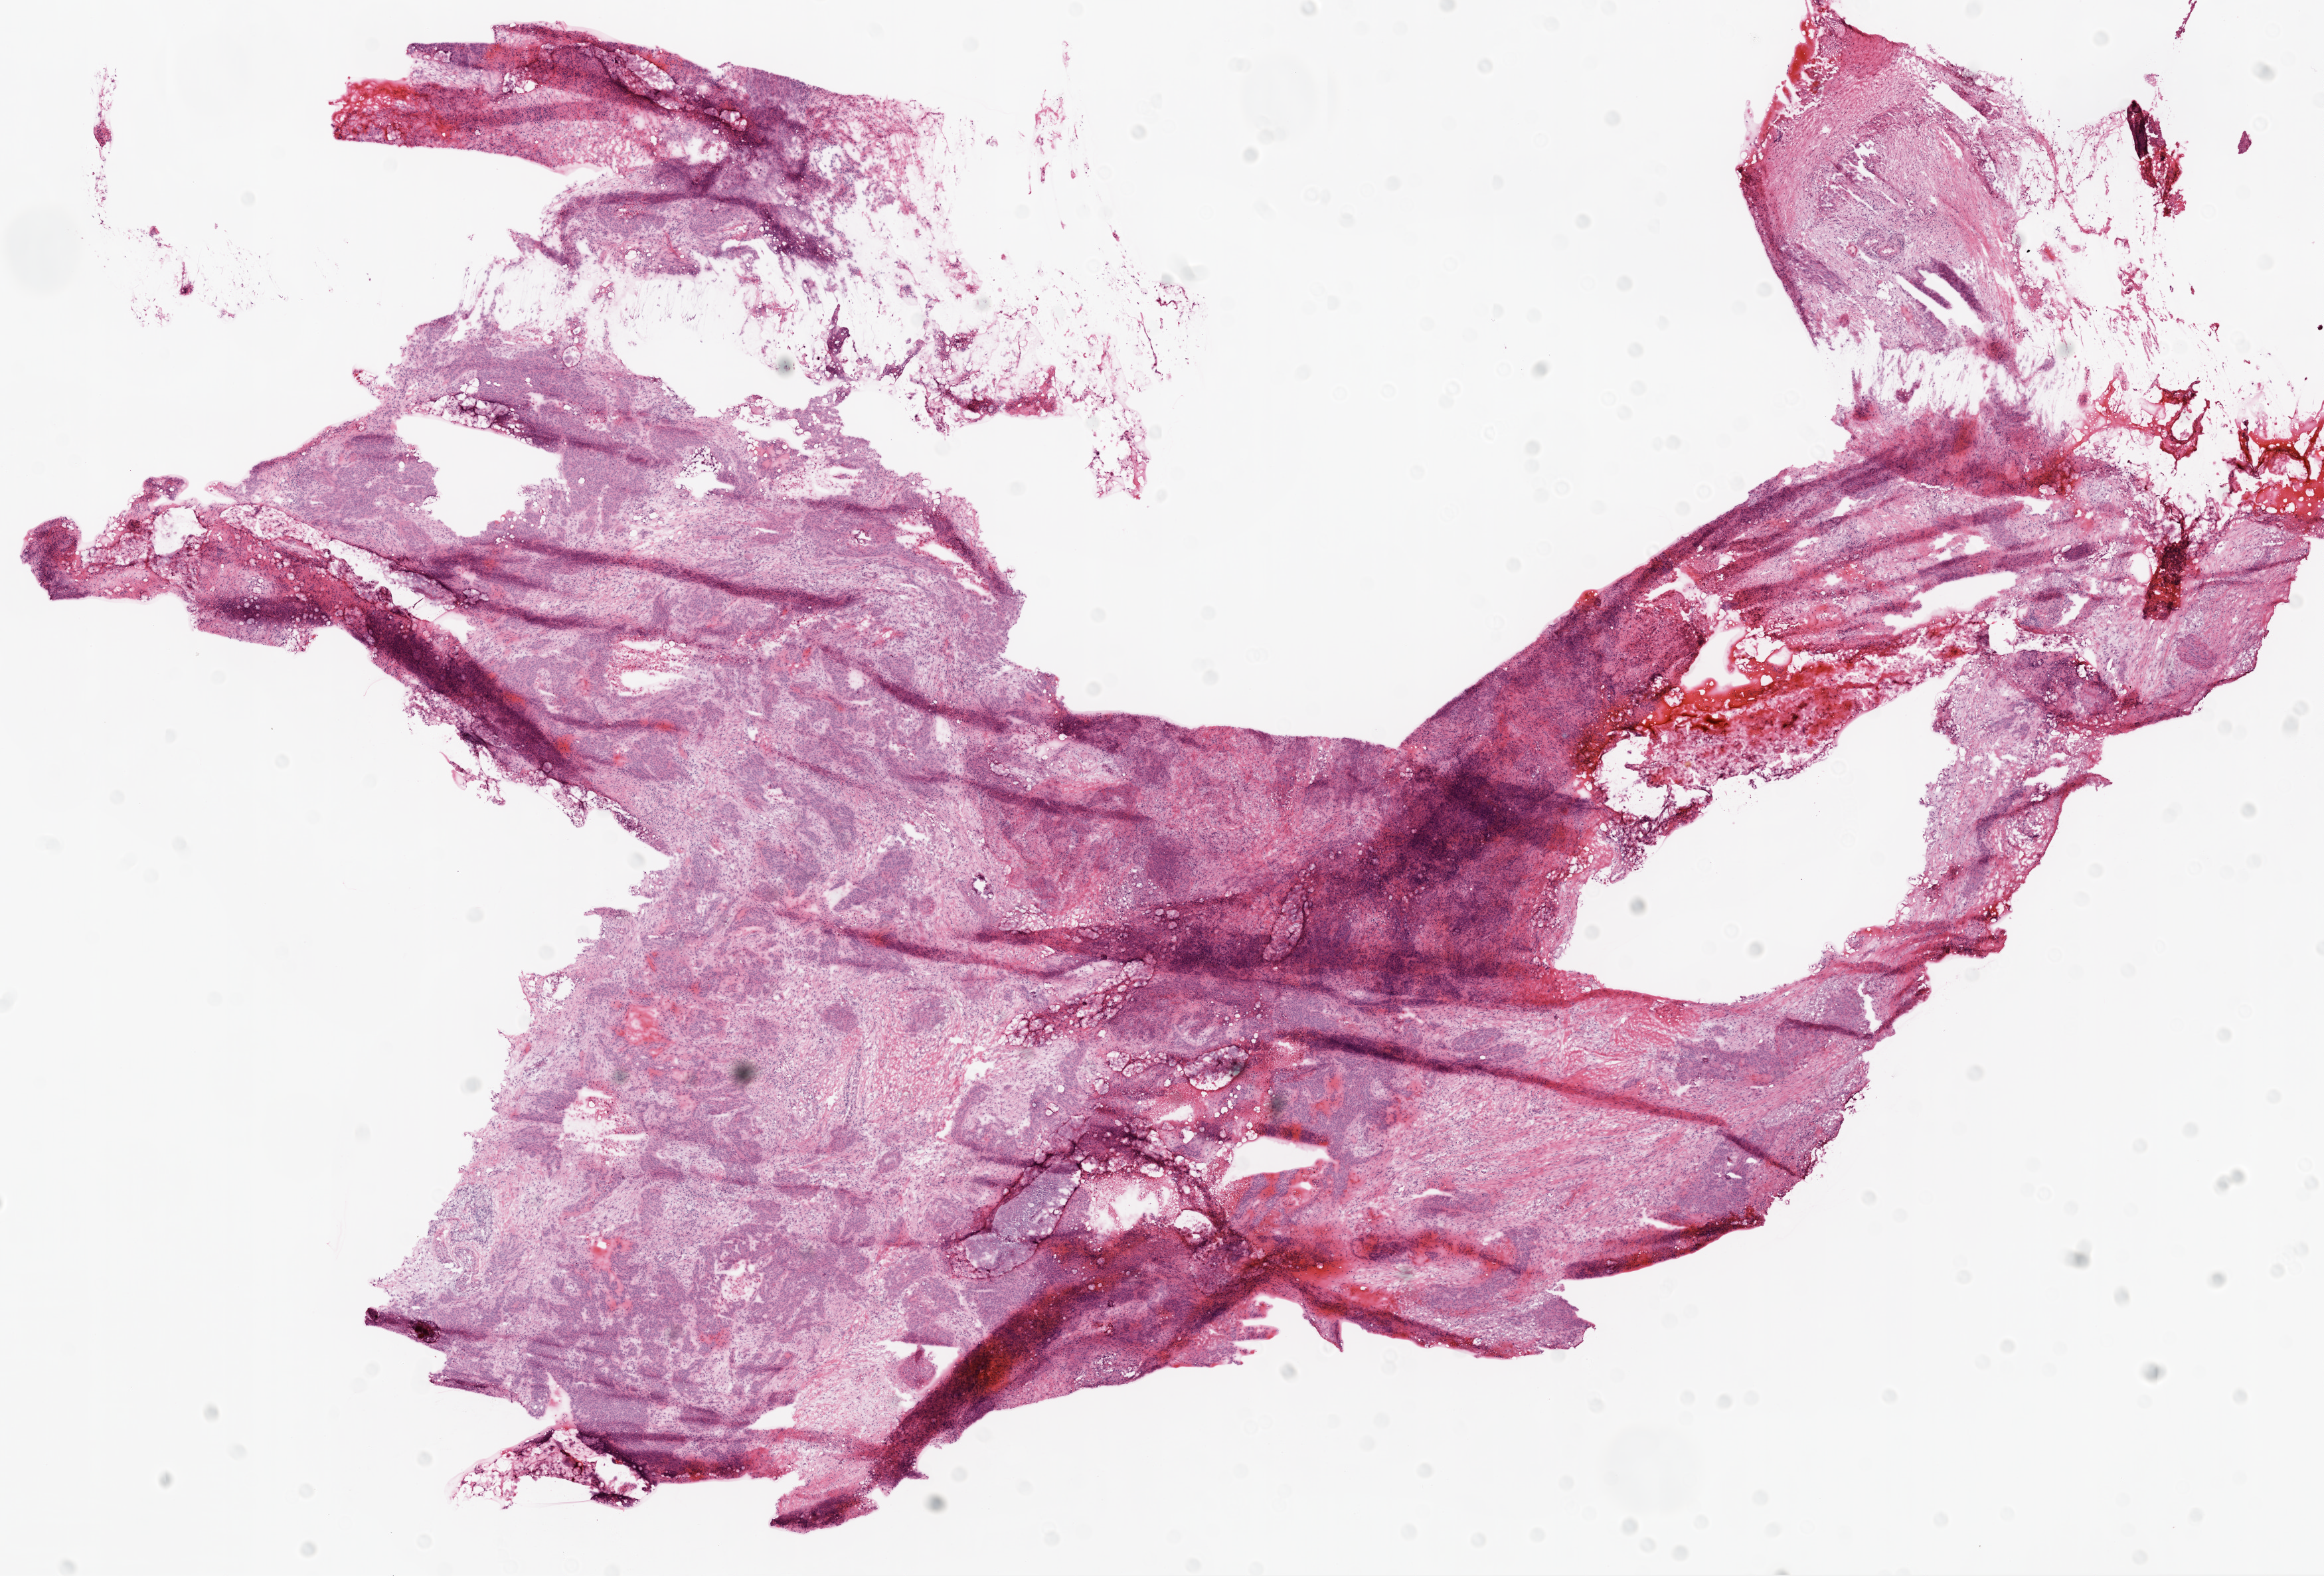
Hematoxylin and eosin (H&E) stained whole-slide image, shown as a low-resolution overview of the whole scanned area (about 14.0 x 9.5 mm, slide scanned at 20x), frozen section from the top of the tissue portion, ovary, primary tumour sample. Female patient; age at initial diagnosis 65 years. Histologic grade: G3 (poorly differentiated). Pathologist review of this section (percent, as recorded): tumour cells 55%, tumour nuclei 70%, normal cells 0%, stromal cells 40%, necrosis 5%.
Diagnosis: Serous cystadenocarcinoma, NOS. FIGO stage: IIIC. Laterality: right.